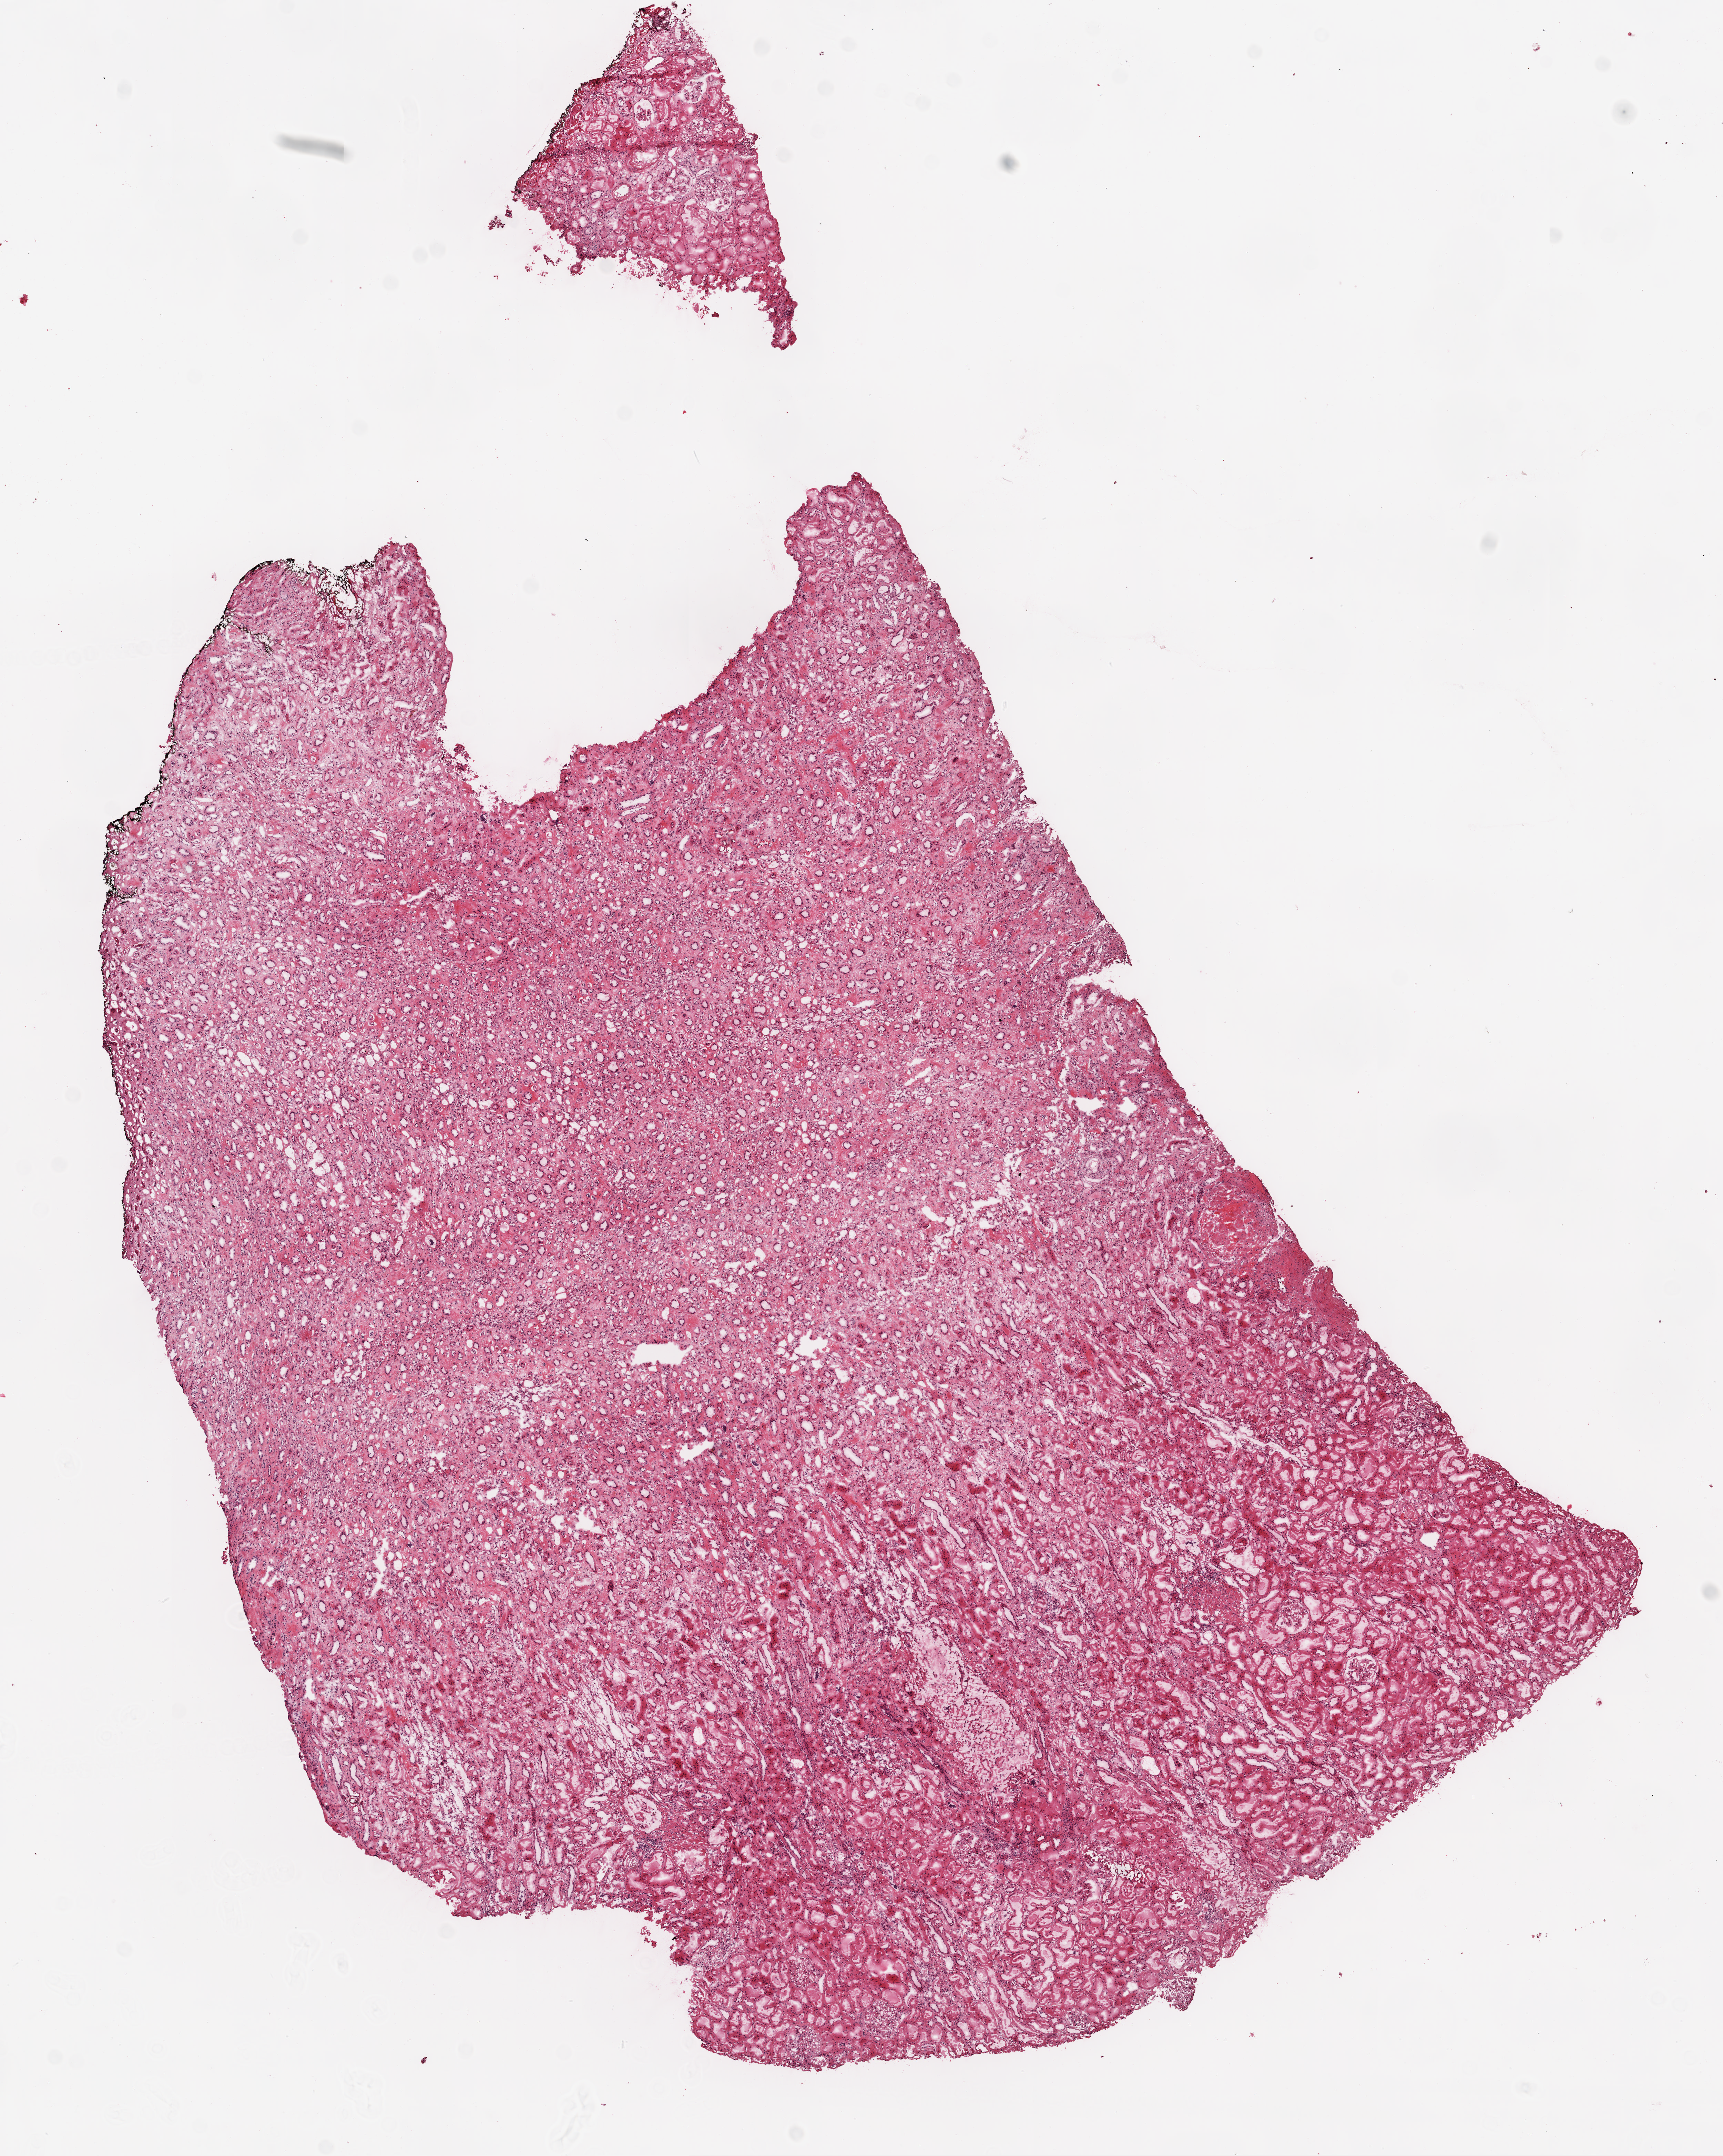
Digitized H&E tissue section (whole slide) — low-resolution overview of the scanned area, about 10.0 x 12.6 mm; frozen section from the top of the tissue portion; solid tissue normal (non-tumour tissue) sample from the kidney. Male patient; age at initial diagnosis 75 years.
This section: solid tissue normal (non-tumour) sample from the same patient. Patient diagnosis: Clear cell adenocarcinoma, NOS.